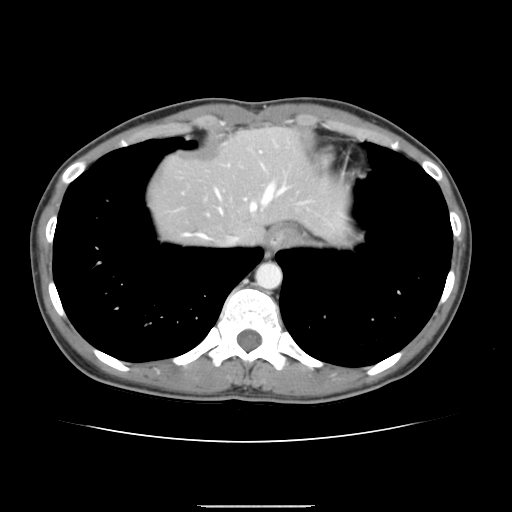
Contrast-enhanced abdominal CT, one axial slice; slice 127 of 150 in the series (ordered by position); 120 kVp; intravenous contrast given; soft-tissue window (W 400 / L 40 HU); 2.5 mm slice thickness; 512 × 512 image matrix, field of view 324 × 324 mm. Female patient, age 32 years. Case-level facts recorded for this patient, not image findings: diagnosis: colorectal cancer liver metastases, imaged before liver resection; multiple liver metastases: yes; largest metastasis: 0.7 cm; disease in both lobes: no.
Structures marked on this image (outlined manually by an expert reader):
- hepatic veins: bounding box <185,183,286,244> (left, top, right, bottom; pixels)
- liver: <150,128,345,245>
- planned liver remnant (the part of the liver to remain after resection): <150,128,344,243>
- portal vein (with intrahepatic branches): <260,151,263,166>